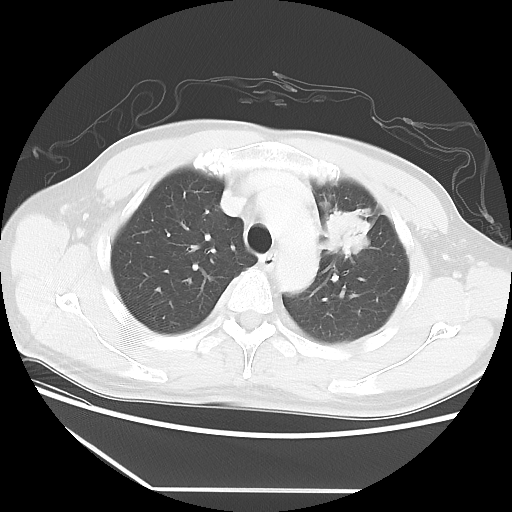
Chest CT, one axial slice. Position 42 of 56 along the scan axis. Reconstruction kernel LUNG. Lung window (W 1500 / L -600 HU). 5 mm slice thickness. 512 × 512 image matrix, field of view 373 × 373 mm. Male patient, age 53 years. From the clinical record (not read from this slice): clinical TNM (as recorded): T2a N1 M1b.
Outlined on this slice (rectangle marked by the reading radiologist):
- lung tumour (recorded histology: adenocarcinoma): bounding box (x1, y1, x2, y2) in pixels: (322, 203, 372, 262)